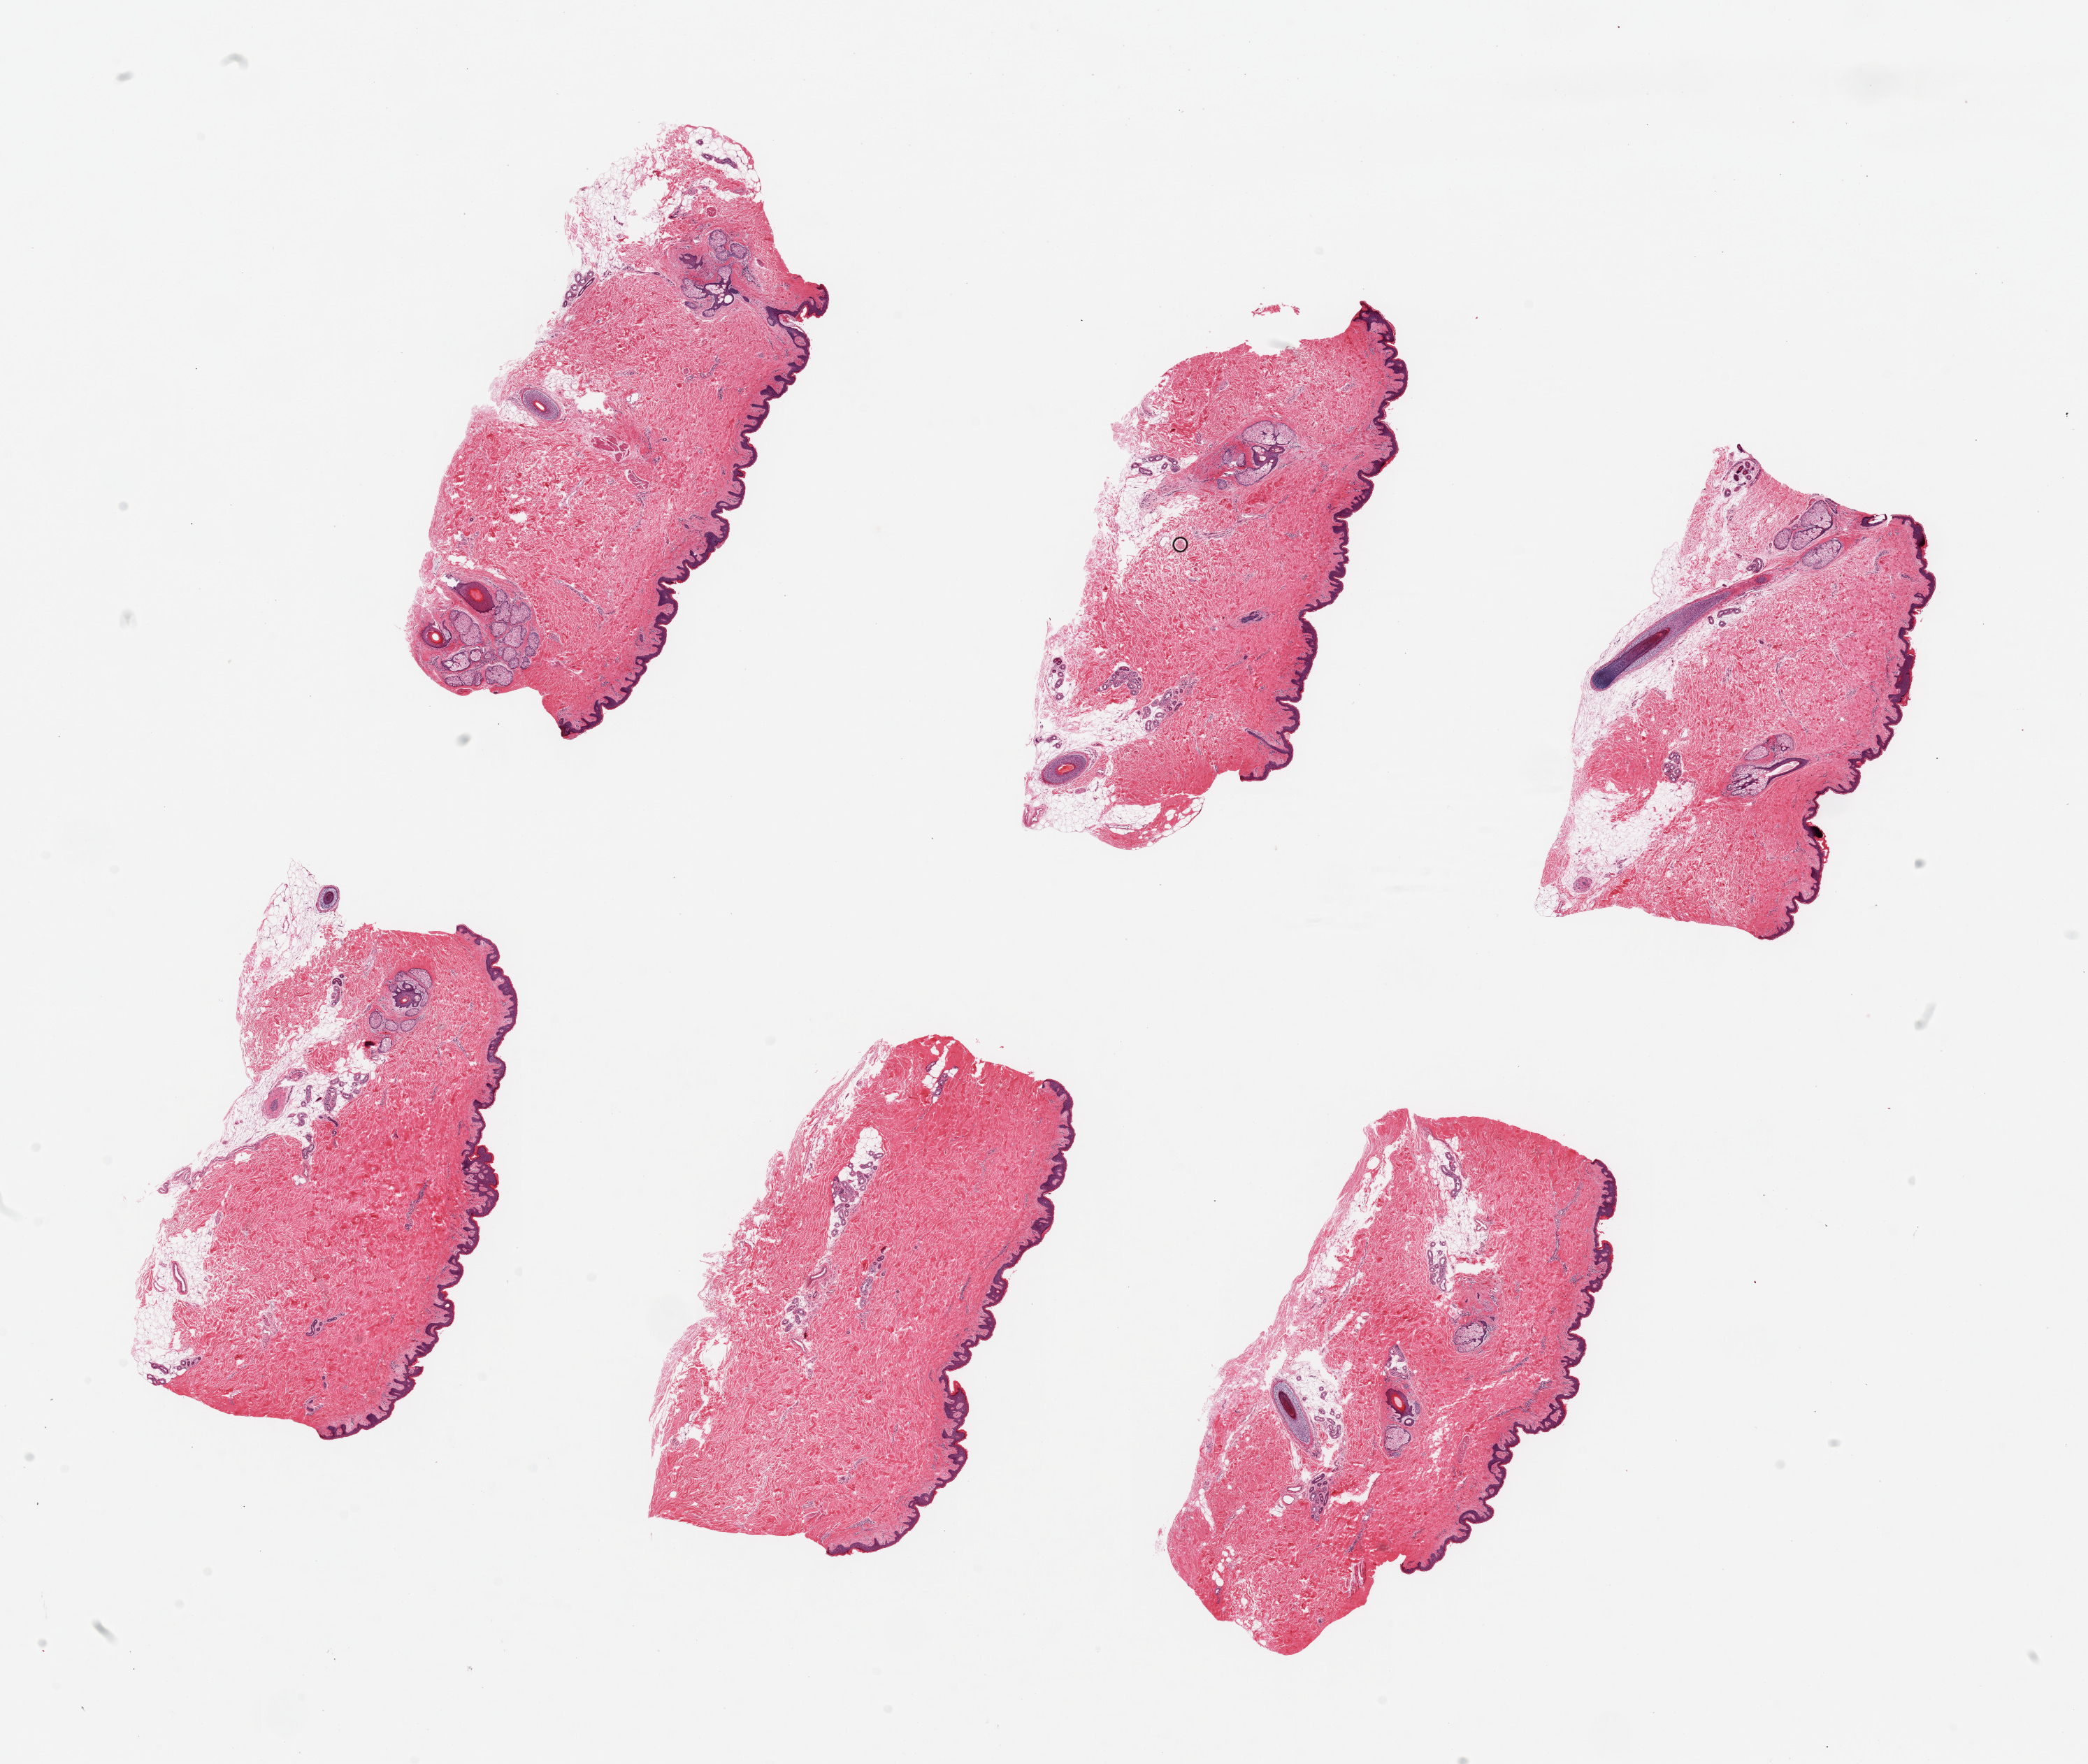
Digitized haematoxylin and eosin-stained section — low-resolution overview of the scanned area, about 23.6 x 20.0 mm (from a 20x scan), PAXgene-fixed, paraffin-embedded tissue, sampled site (target tissue): skin of suprapubic region, tissue donor sample. Donor sex: male.
Pathologist's review note for this sample: 6 pieces ~6x3mm; Squmous epithelium is ~2% thickness; prominent sebacious glands.